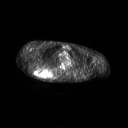
FDG PET of an extremity soft-tissue mass (from a PET/CT study), one axial slice; position 185 of 267 along the scan axis; 3.27 mm slice thickness; 128 × 128 image matrix, field of view 700 × 700 mm. Male patient, age 61 years. Case-level facts recorded for this patient, not image findings: histological type: pleiomorphic spindle cell undifferentiated; grade: high; site of the primary tumour: right parascapusular.
Outlined on this slice (expert contour drawn on MRI and transferred to this co-registered scan by the dataset authors):
- gross tumour volume including surrounding oedema: box from (x=33, y=67) to (x=58, y=79) px
- gross tumour volume (mass): (x=34, y=68)–(x=51, y=78)